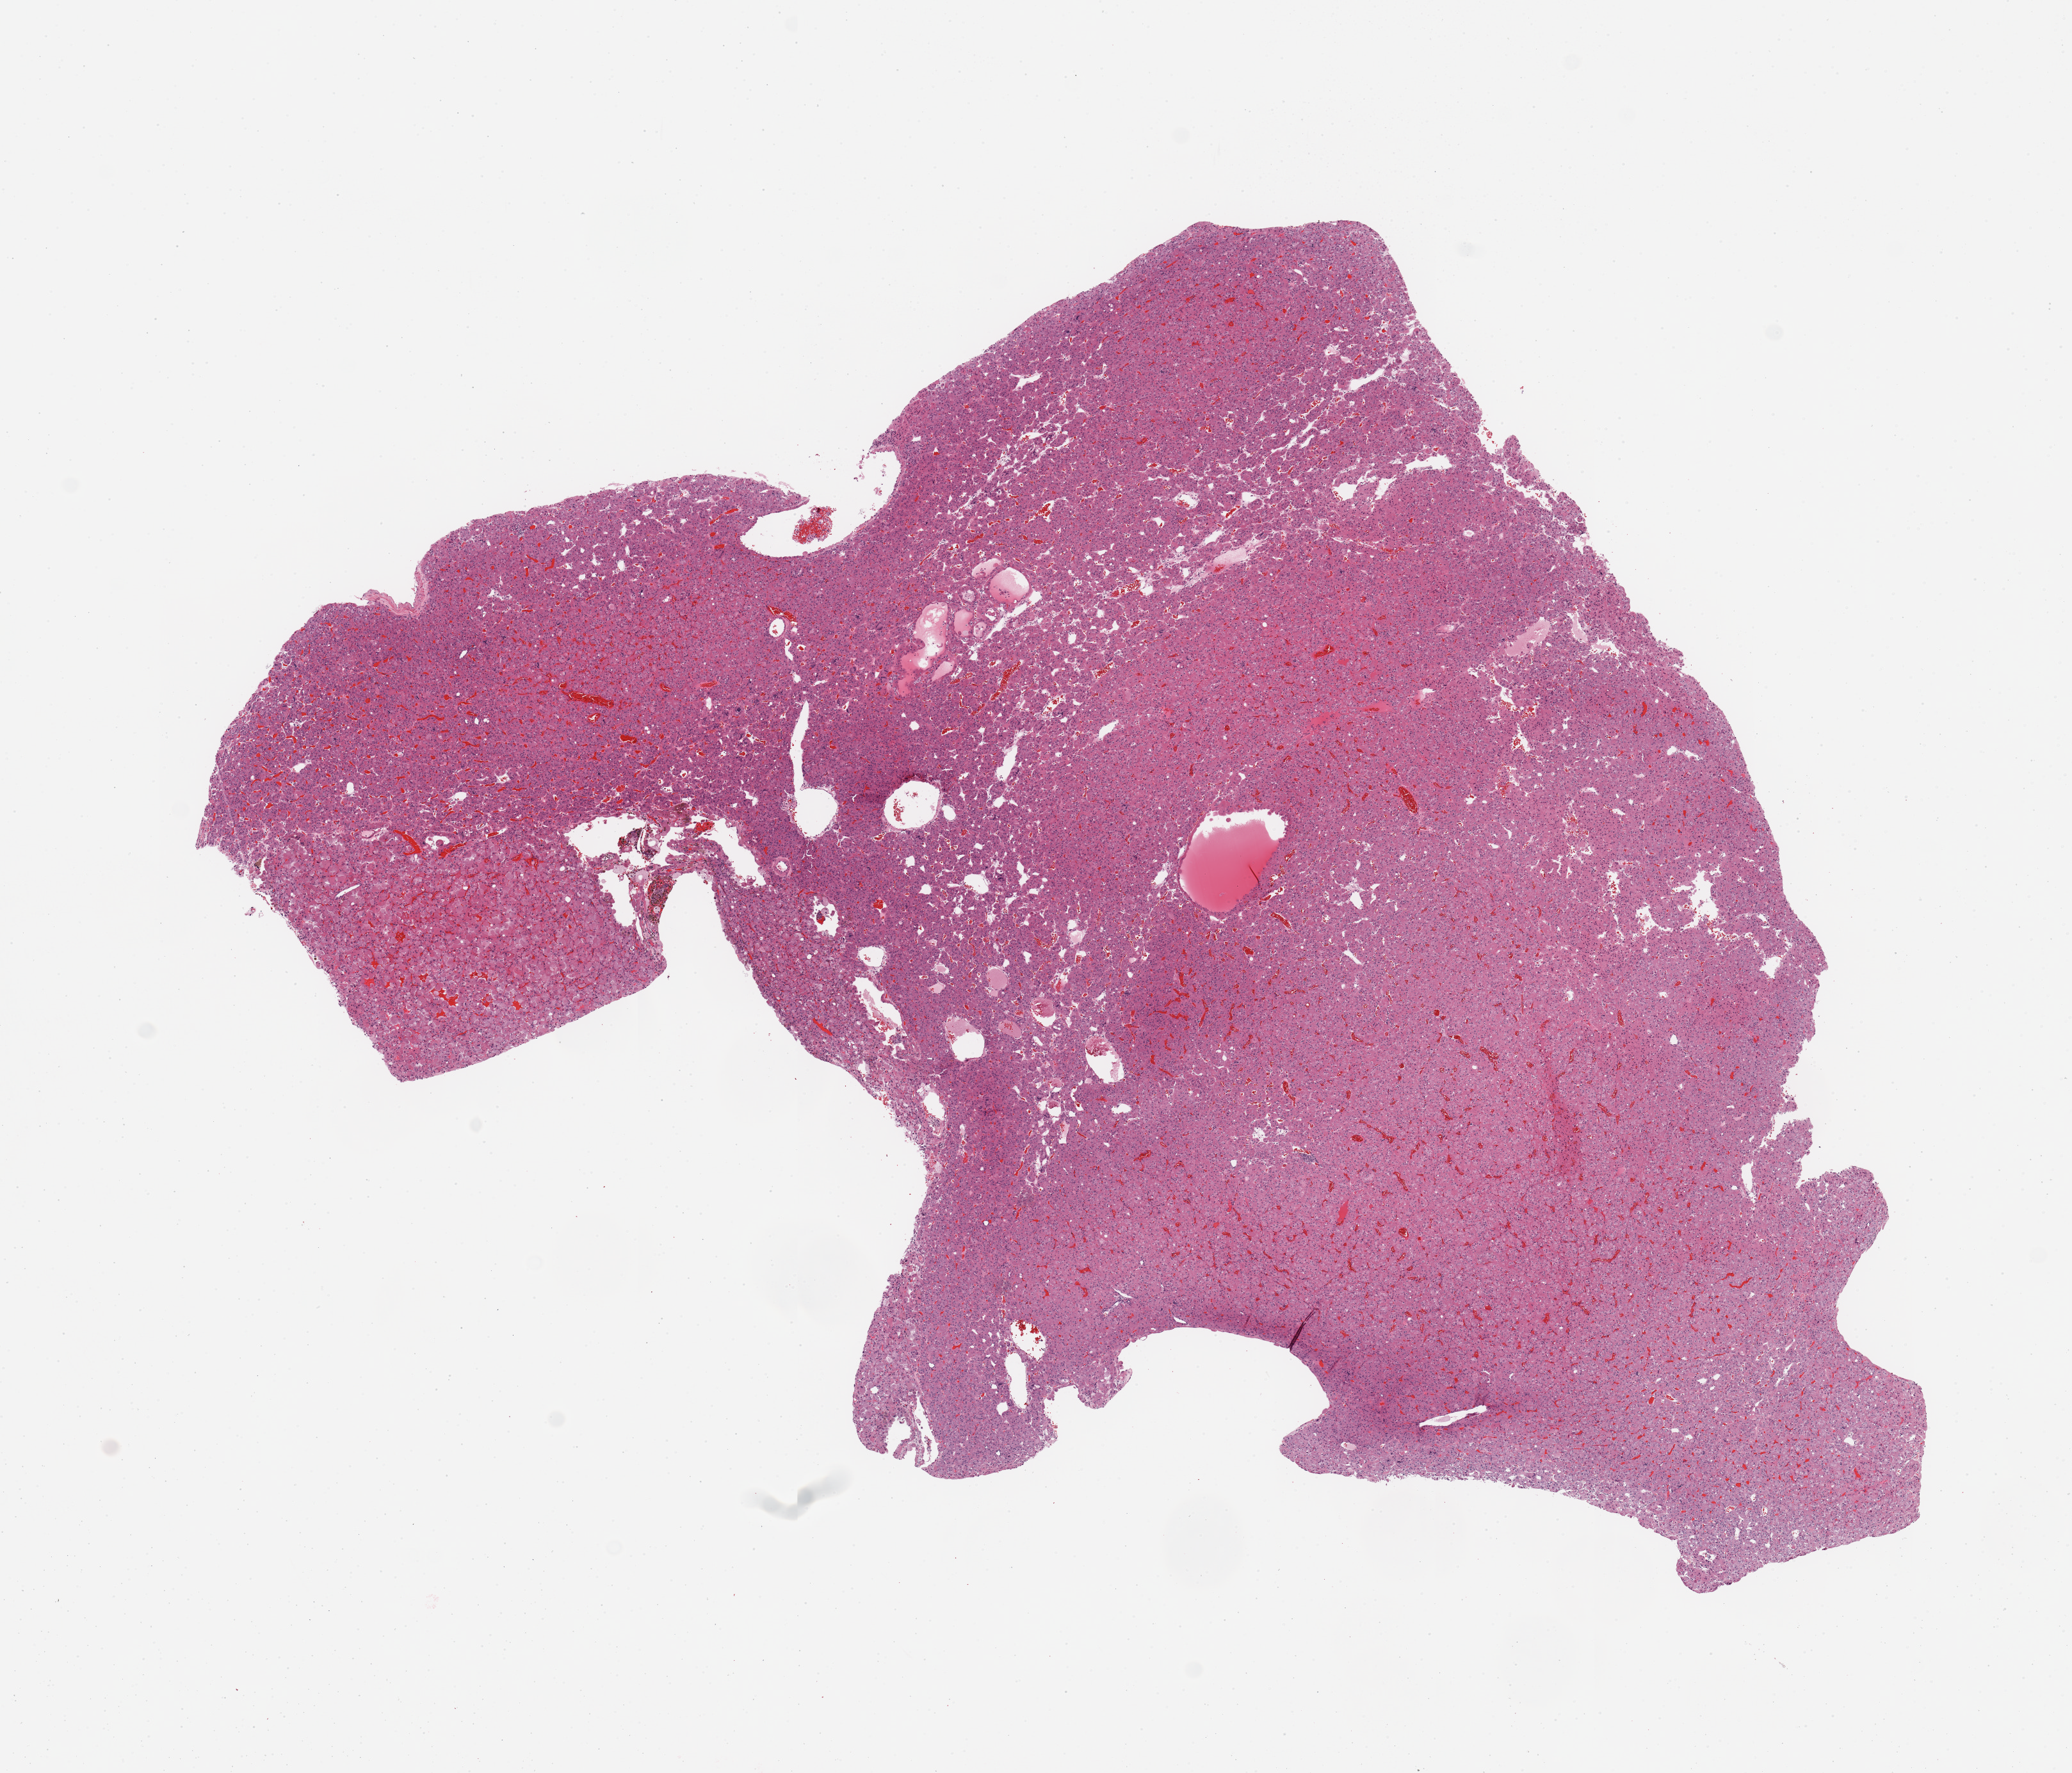
Whole-slide histology image, H&E — shown as a low-resolution overview of the whole scanned area (about 12.8 x 11.0 mm, acquisition: 20x scan); tumour tissue sample, sampled site: kidney. 73-year-old female patient. Histologic grade: G1 (well differentiated). Composition of this section per pathologist review: tumour nuclei 95%, necrosis 0%.
Diagnosis: Renal cell carcinoma, NOS. AJCC pathologic stage: I.